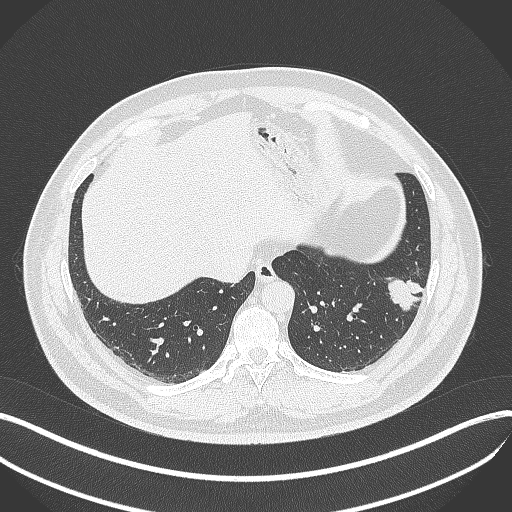
Chest CT, one axial slice; slice 116 of 429 in the series (ordered by position); reconstruction kernel B70f; lung window (W 1500 / L -600 HU); 512 × 512 image matrix. Male patient, age 39 years. Case-level facts recorded for this patient, not image findings: clinical TNM (as recorded): T2a N0 M0; histopathological grade: G2-3.
Structures marked on this image (rectangle marked by the reading radiologist):
- lung tumour (recorded histology: adenocarcinoma): bounding box (x1, y1, x2, y2) in pixels: (380, 275, 430, 314)